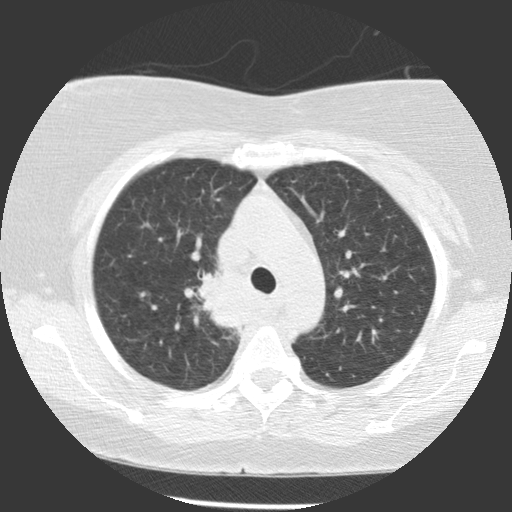
Low-dose screening chest CT, one axial slice; reconstruction kernel STANDARD; 140 kVp; lung window (W 1500 / L -600 HU); 512 × 512 image matrix, field of view 320 × 320 mm.
Outlined on this slice (outlined manually by an expert reader):
- lesion 1 (tumor, upper lobe of right lung): bounding box <199,272,239,329> (left, top, right, bottom; pixels)